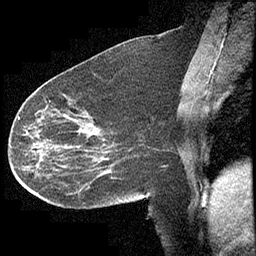
Breast MRI (dynamic contrast-enhanced), one sagittal slice; position 175 of 232 along the scan axis; dynamic contrast-enhanced study with each time point stored as its own series, time point 2 of 4 at this slice position (early post-contrast, ordered by acquisition time); 1.5 T; TE 4.2 ms, TR 6.7 ms; 3 mm slice thickness; 256 × 256 image matrix. Female patient, age 63 years. Case-level facts recorded for this patient, not image findings: setting: breast cancer imaged before/during neoadjuvant chemotherapy; receptor status: triple-negative.
Outlined on this slice (semi-automatic segmentation, software-assisted and operator-edited):
- analysis volume of interest (the breast-tissue region the enhancement analysis was run in; not a lesion): bounding box (x1, y1, x2, y2) in pixels: (13, 90, 140, 210)
- tumour enhancement mask (voxels above the 70 % enhancement threshold inside the analysis volume of interest): (18, 117, 38, 167)